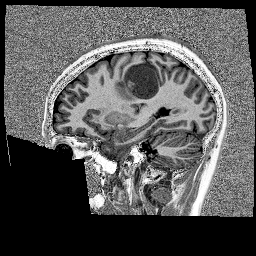
Brain MRI from a brain-tumour surgery series, one sagittal slice. Position 62 of 176 along the scan axis. 1 mm slice thickness. 256 × 256 image matrix. Case-level facts recorded for this patient, not image findings: histopathology: Glioblastoma; WHO grade: 4; IDH mutation: no; tumour location: Left Frontal.
Structures marked on this image (expert manual segmentation):
- tumour: bounding box [x1, y1, x2, y2] px = [120, 58, 157, 96]